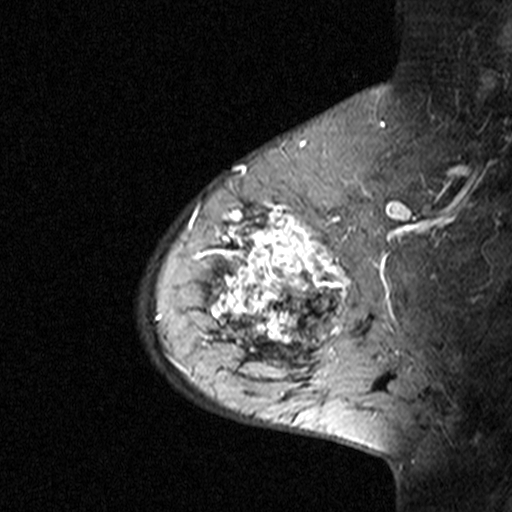
Breast MRI (dynamic contrast-enhanced), one sagittal slice; position 30 of 44 along the scan axis; dynamic contrast-enhanced study with each time point stored as its own series, time point 3 of 4 at this slice position (ordered by acquisition time); 1.5 T; TE 4.5 ms, TR 11 ms; 3 mm slice thickness; 512 × 512 image matrix, field of view 200 × 200 mm. Female patient, age 65 years. Case-level facts recorded for this patient, not image findings: setting: breast cancer imaged before/during neoadjuvant chemotherapy; receptor status: HER2-positive.
Structures marked on this image (semi-automatic segmentation, software-assisted and operator-edited):
- analysis volume of interest (the breast-tissue region the enhancement analysis was run in; not a lesion): box from (x=182, y=190) to (x=353, y=361) px
- tumour enhancement mask (voxels above the 90 % enhancement threshold inside the analysis volume of interest): (x=190, y=202)–(x=351, y=351)